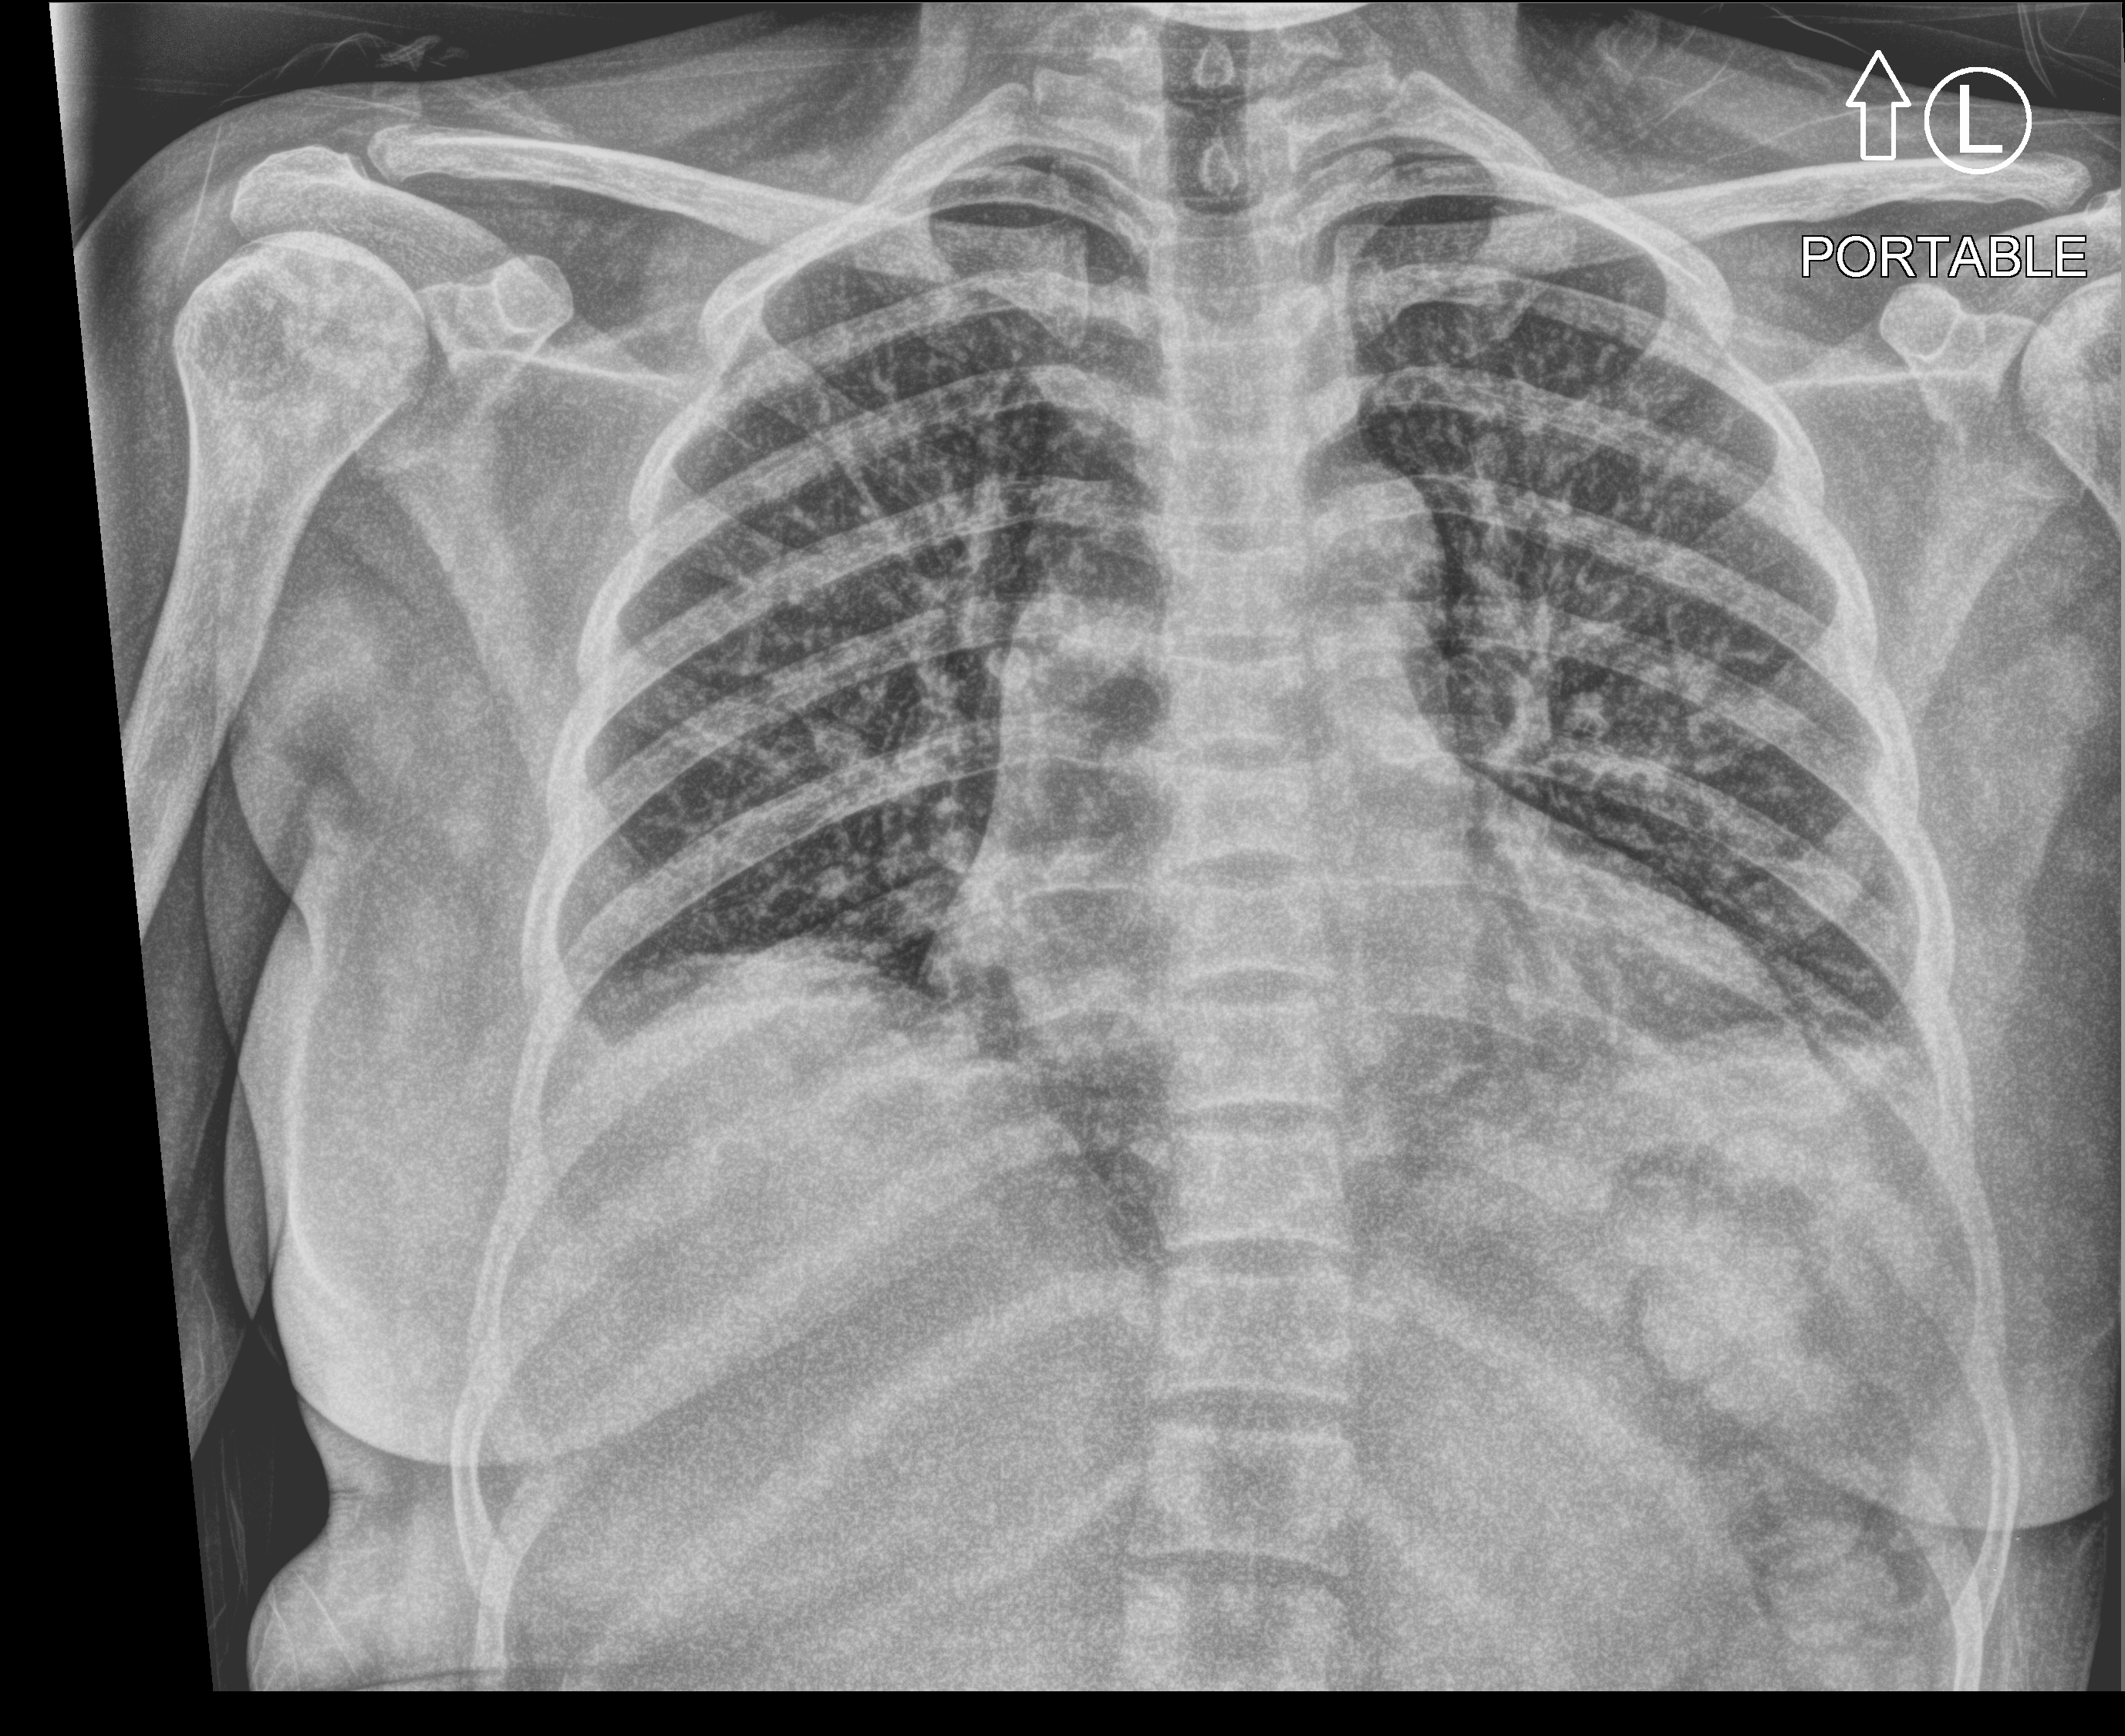
Chest X-ray (portable); anteroposterior (AP) projection. Female patient hospitalised with COVID-19, age 18–59 years.
From the hospital-stay record, not from the radiograph (when in the stay this image was taken is not recorded): diabetes (admission record): no; mechanically ventilated during this hospital stay: no; admitted to intensive care during this hospital stay: no.